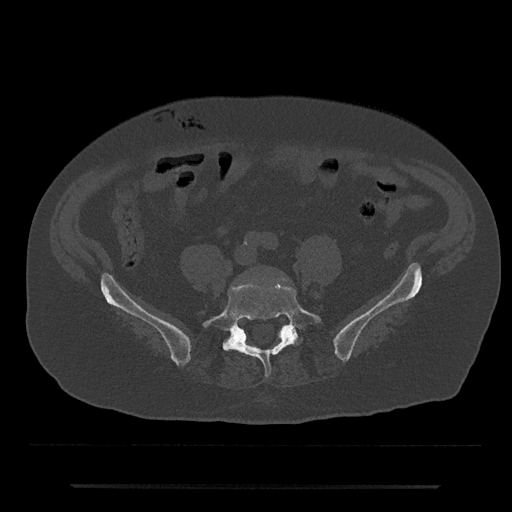
CT including the spine, one axial slice; position 290 of 797 along the scan axis; 120 kVp; bone window (W 1800 / L 400 HU); 0.5 mm slice thickness; 512 × 512 image matrix, field of view 434 × 434 mm. Patient: male, 80 years. From the clinical record (not read from this slice): primary cancer: prostate; vertebrae with lytic lesions (as recorded): L1, T11.
Outlined on this slice (semi-automatic segmentation, software-assisted and operator-edited):
- L5 vertebra: bounding box (x1, y1, x2, y2) in pixels: (203, 284, 321, 377)